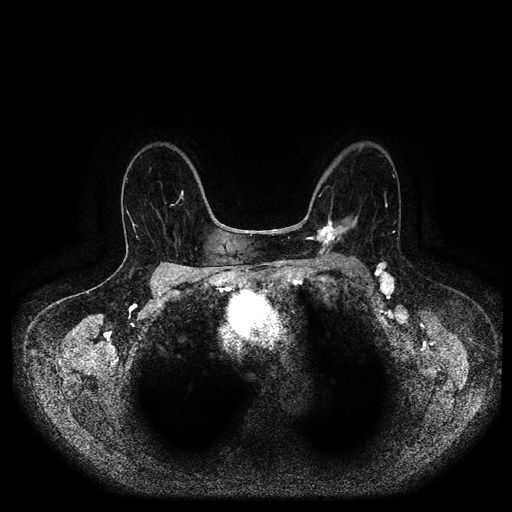
Breast MRI (dynamic contrast-enhanced, multi-phase), one axial slice; dynamic contrast-enhanced series, time point 2 of 5 at this slice position (early post-contrast); 1.5 T; TE 2.6 ms, TR 5.2 ms; 2 mm slice thickness; 512 × 512 image matrix, field of view 380 × 380 mm. Female patient, age 69 years.
Outlined on this slice (semi-automatically segmented with operator editing):
- breast lesion (labelled 'tumour' in the annotation; benign lesions carry a separate 'benign' label): bounding box <305,214,358,257> (left, top, right, bottom; pixels)